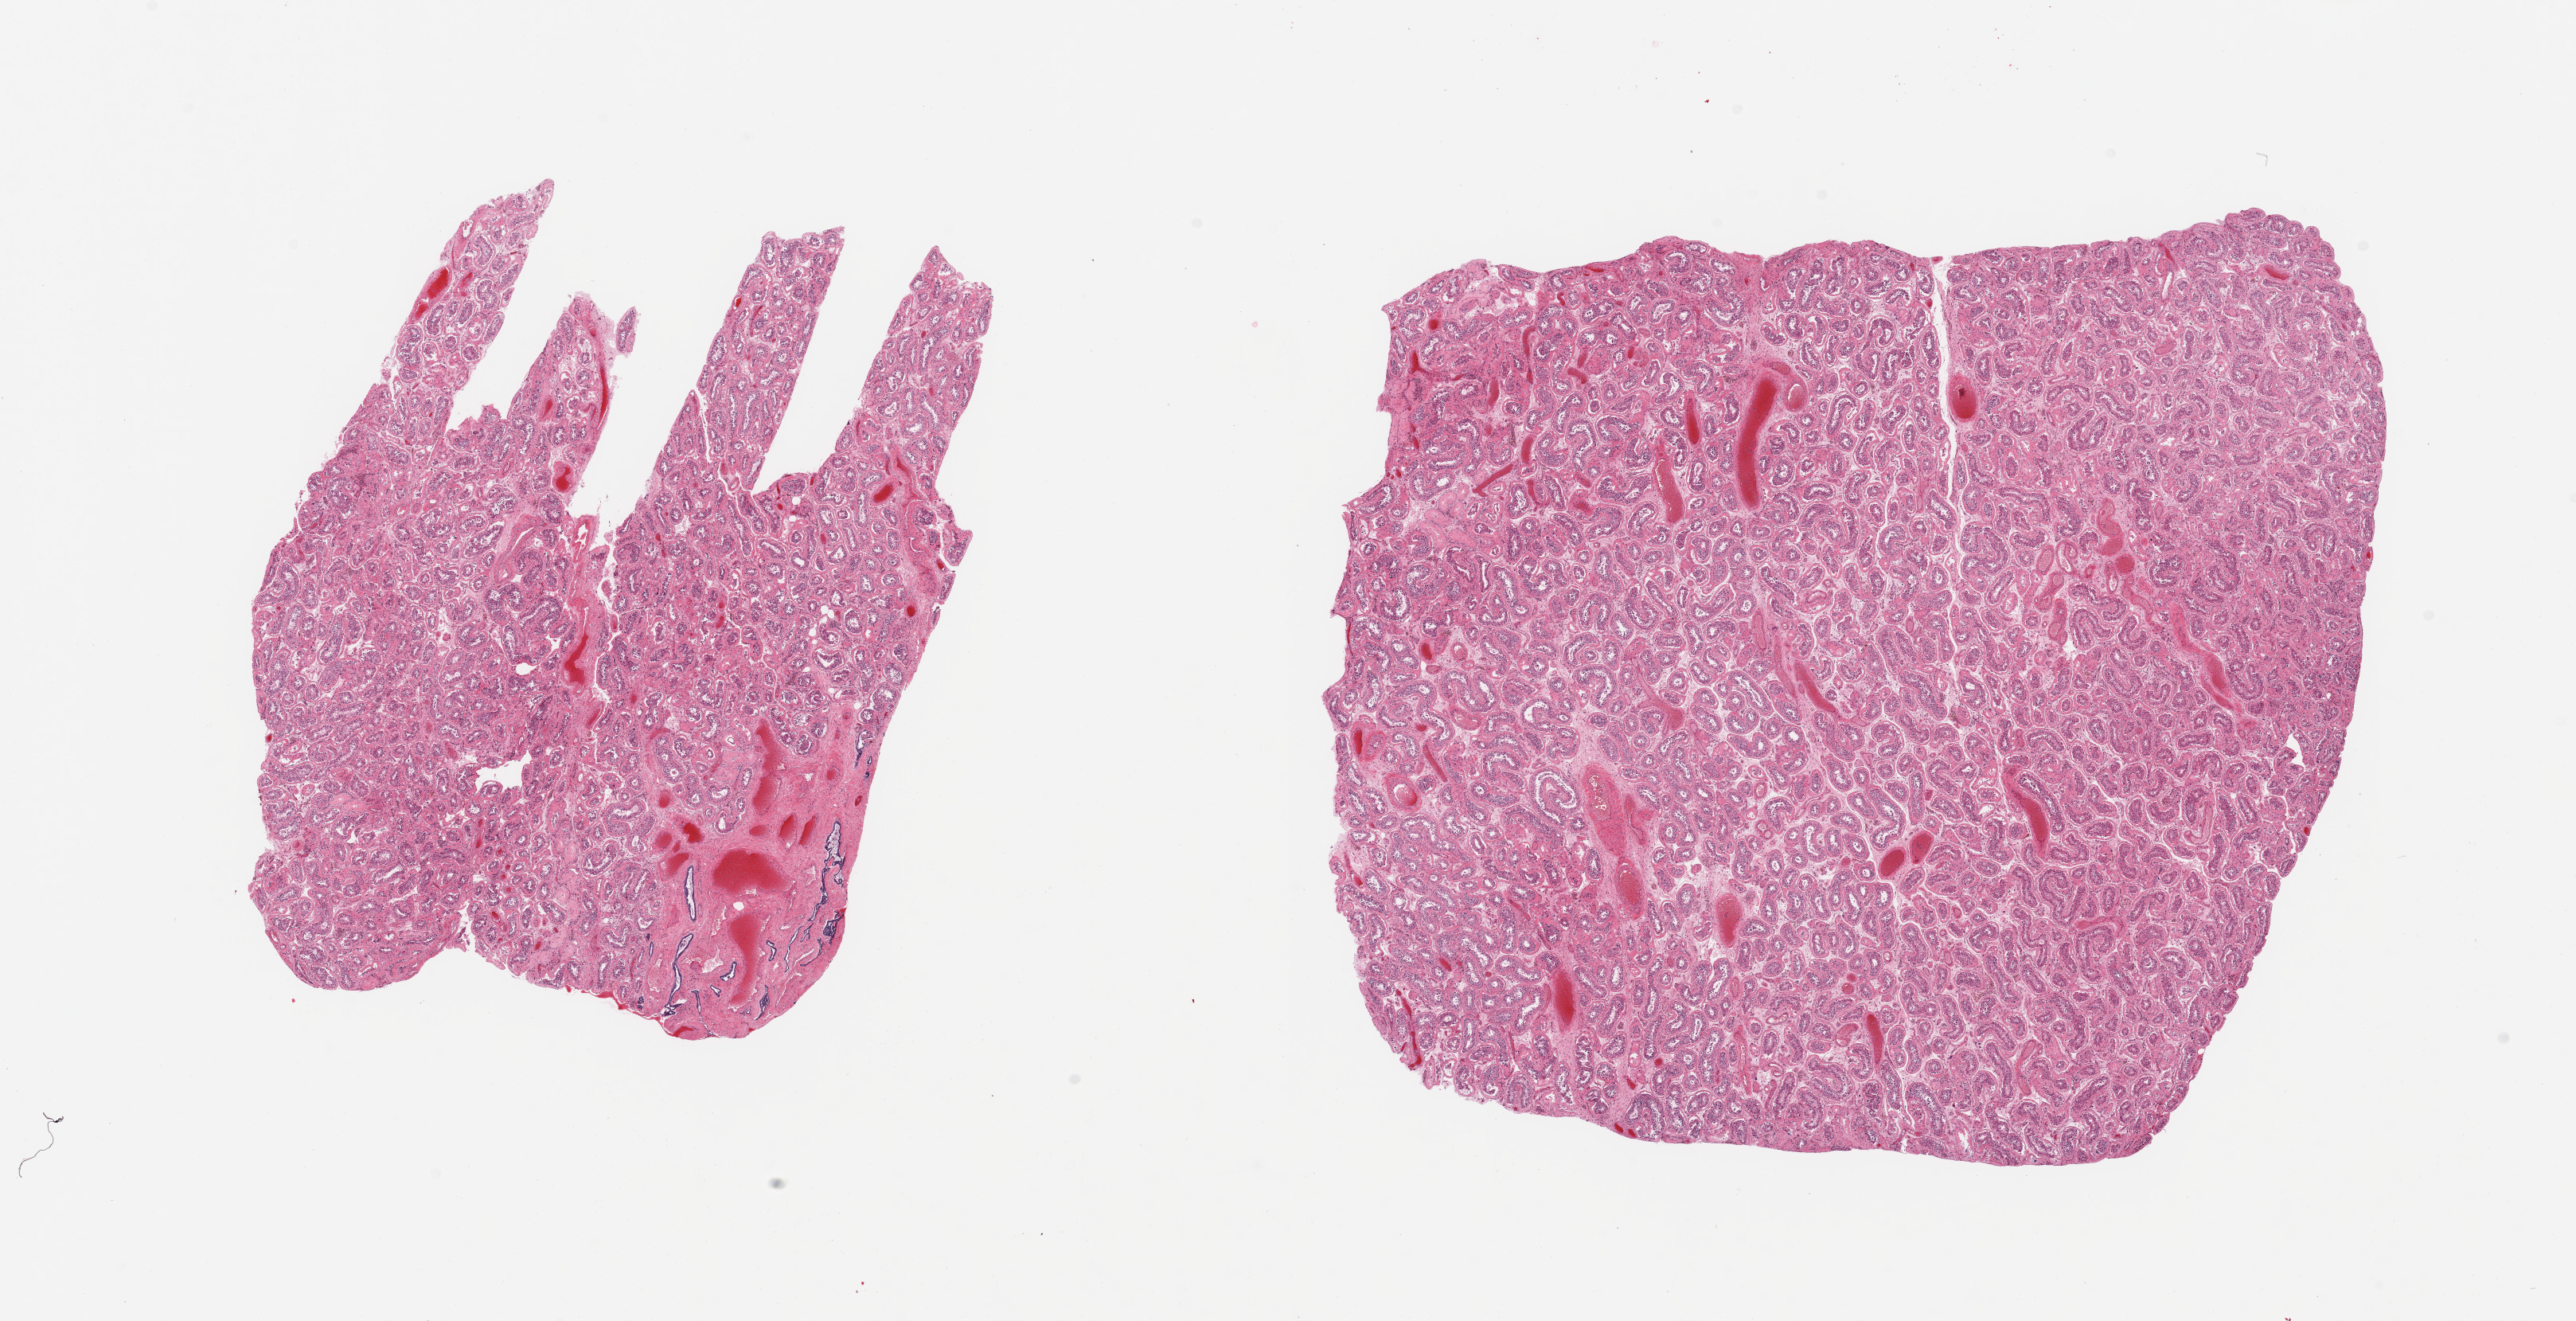
Haematoxylin and eosin whole-slide image, brightfield — a low-resolution overview of the entire scanned area, about 25.6 x 13.1 mm (from a 20x scan), PAXgene-fixed paraffin-embedded (PFPE) section, sampled site (target tissue): testis, tissue donor sample. Donor sex: male.
Pathologist's review note for this sample: 2 pieces; moderate reduction in mature spermatogenesis; no scarring.